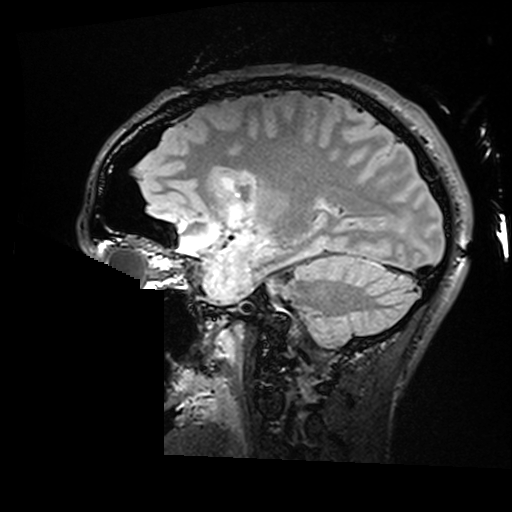
Brain MRI from a brain-tumour surgery series, one sagittal slice; slice 107 of 176 in the series (ordered by position); T2 FLAIR; 512 × 512 image matrix. Case-level facts recorded for this patient, not image findings: histopathology: Astrocytoma; WHO grade: 2; IDH mutation: yes; tumour location: Right Insular.
Outlined on this slice (expert manual segmentation):
- residual tumour: bounding box (x1, y1, x2, y2) in pixels: (222, 177, 234, 188)